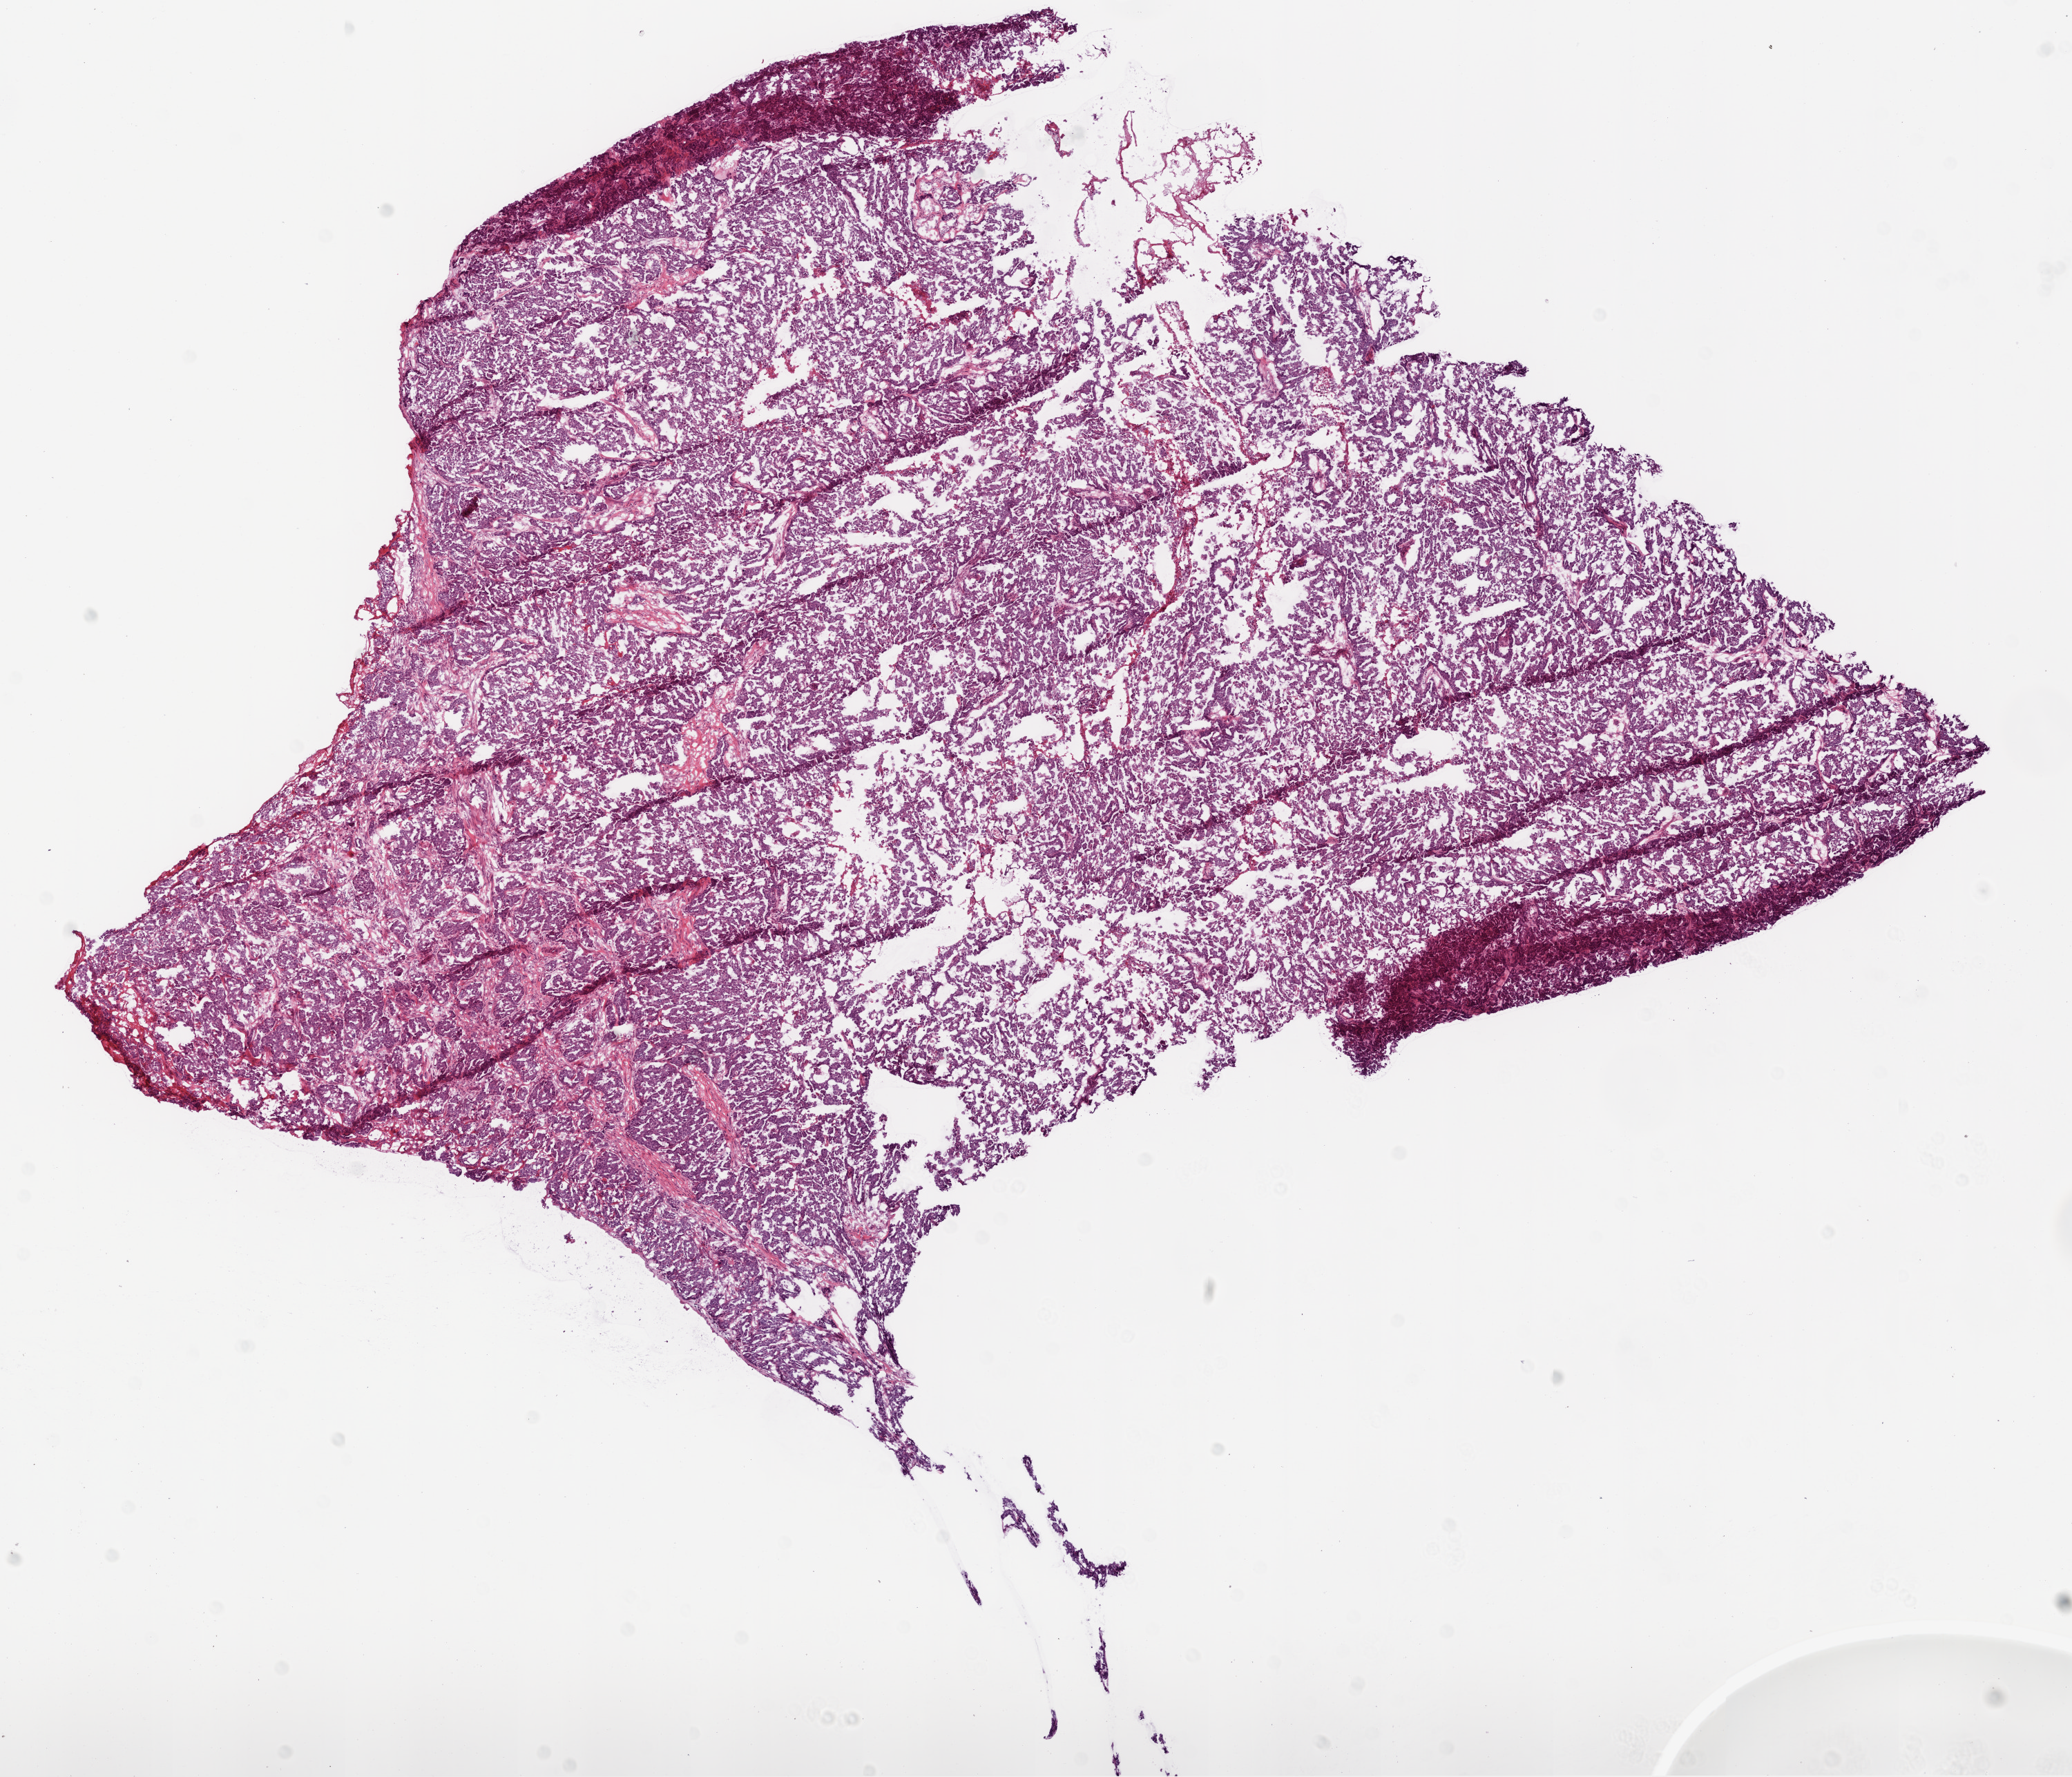
Hematoxylin and eosin (H&E) stained whole-slide image — low-resolution overview of the scanned area, about 12.0 x 10.3 mm, frozen section from the bottom of the tissue portion, ovary, primary tumour sample. Female, age 77 years at initial diagnosis. Histologic grade: G3 (poorly differentiated). Slide review estimates, as recorded: tumour cells 90%, tumour nuclei 99%, normal cells 0%, stromal cells 5%, necrosis 5%.
FIGO stage: IIIC. Diagnosis: Serous cystadenocarcinoma, NOS. Laterality: left.